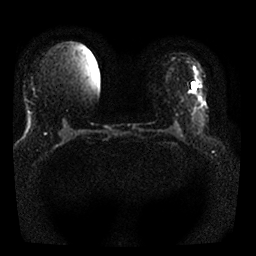
Breast MRI, one axial slice. Position 10 of 25 along the scan axis. Diffusion-weighted series; image 2 of 4 stored at this slice position (different b-values; order by instance number). 1.5 T. 4 mm slice thickness. 256 × 256 image matrix, field of view 320 × 320 mm. Female patient.
Annotated regions visible in this slice (expert manual segmentation):
- tumour on diffusion-weighted imaging: bounding box <192,83,195,90> (left, top, right, bottom; pixels)